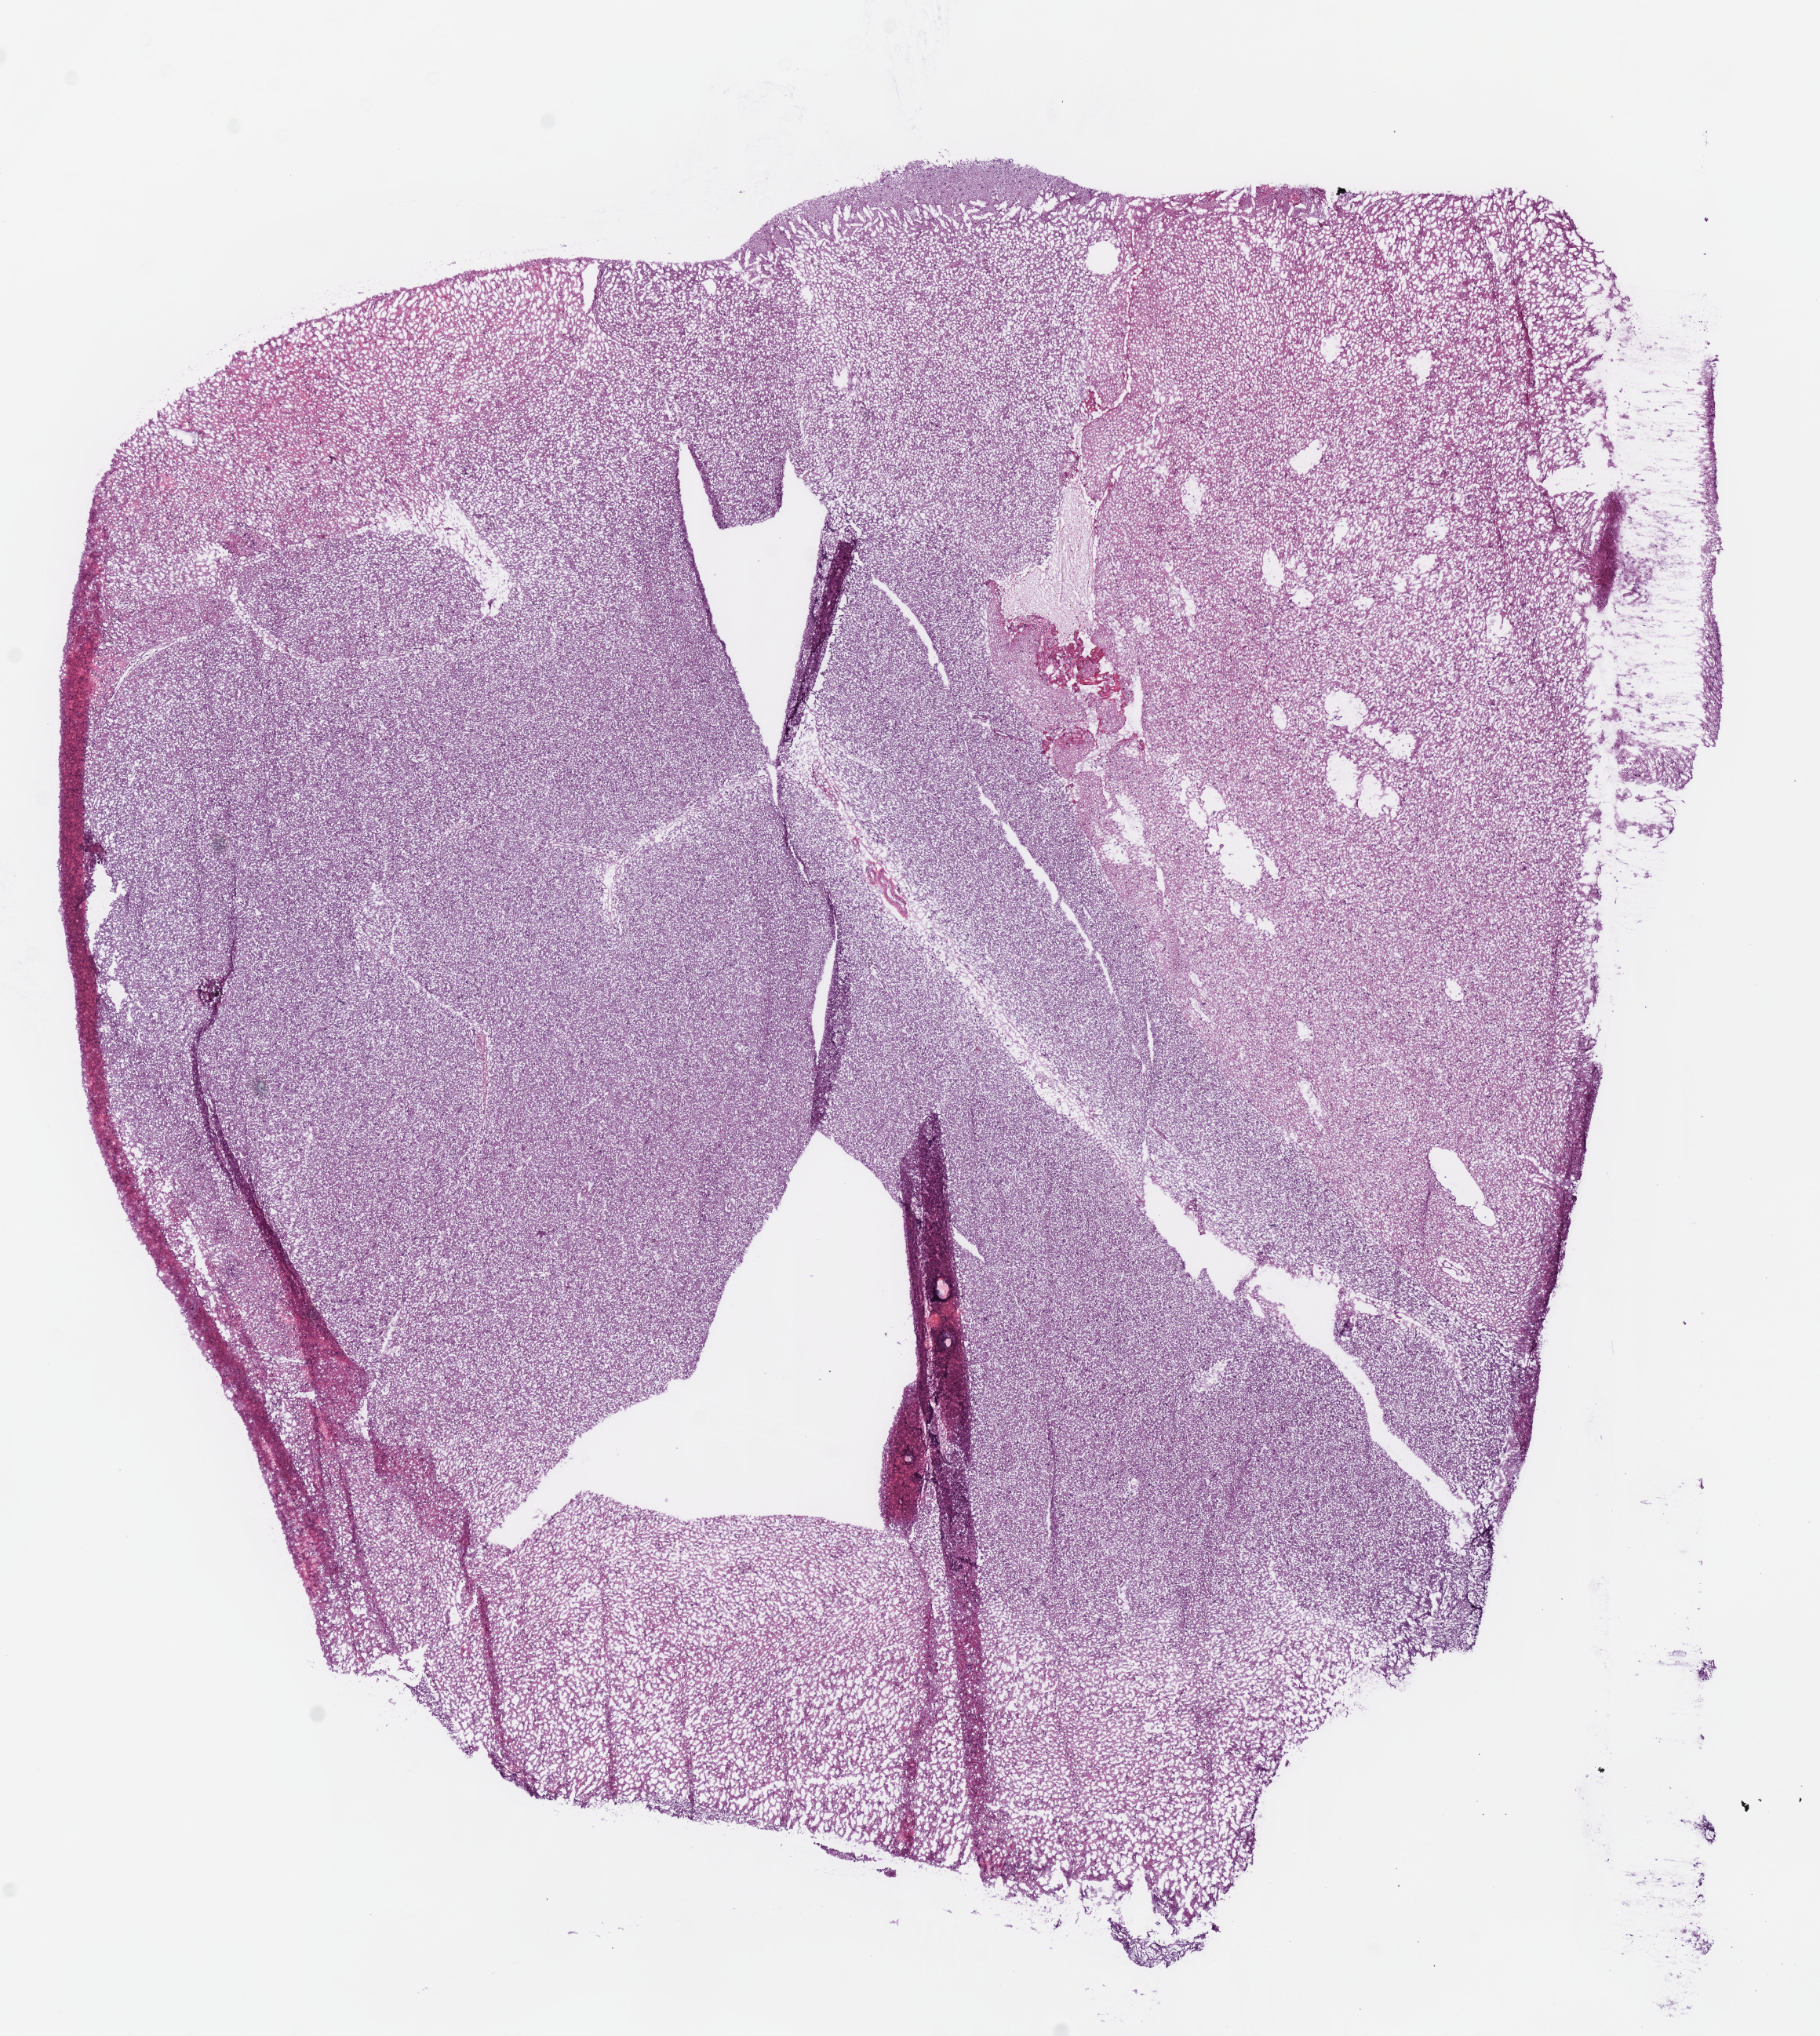
Whole-slide histology image, H&E-stained — shown as a low-resolution overview of the whole scanned area (about 9.1 x 10.2 mm, from a 40x scan), frozen section from the top of the tissue portion, primary tumour sample from the brain. Male patient; age at initial diagnosis 60 years. Histologic grade: G3 (poorly differentiated). Pathologist review of this section (percent, as recorded): tumour cells 100%, tumour nuclei 60%, normal cells 0%, stromal cells 0%, necrosis 0%.
Laterality: right. Diagnosis: Oligodendroglioma, anaplastic (cerebrum).